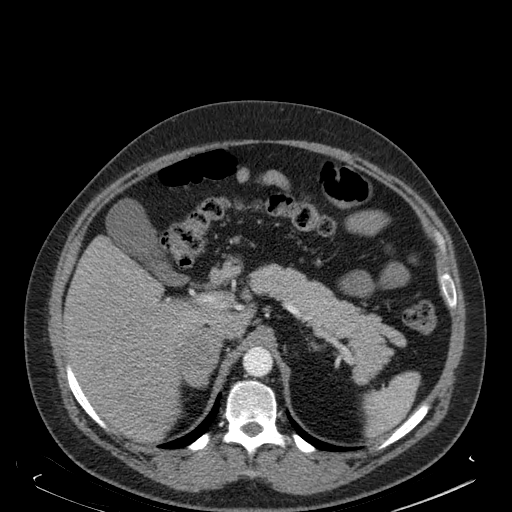
Contrast-enhanced abdominal CT, one axial slice. Position 124 of 181 along the scan axis. Soft-tissue window (W 400 / L 40 HU). 512 × 512 image matrix, field of view 405 × 405 mm. Male patient. From the clinical record (not read from this slice): diagnosis: adrenocortical carcinoma; tumour side: right adrenal; tumour size at pathology: 7.5 cm; Ki-67 index: 25 %; stage (as recorded): 4.
Annotated regions visible in this slice (semi-automatic segmentation, software-assisted and operator-edited):
- mass: bounding box [x1, y1, x2, y2] px = [179, 333, 217, 386]